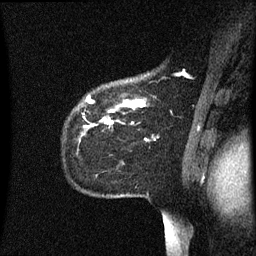
Breast MRI (dynamic contrast-enhanced), one sagittal slice; slice 48 of 60 in the series (ordered by position); dynamic contrast-enhanced series, image 2 of 3 at this slice position (ordered by acquisition); 1.5 T; TE 4.2 ms, TR 8.4 ms; 2.2 mm slice thickness; 256 × 256 image matrix, field of view 200 × 200 mm. Patient: female, 35 years. From the clinical record (not read from this slice): setting: breast cancer imaged before/during neoadjuvant chemotherapy; receptor status: HER2-positive.
Structures marked on this image (semi-automatically segmented with operator editing):
- analysis volume of interest (the breast-tissue region the enhancement analysis was run in; not a lesion): bounding box [x1, y1, x2, y2] px = [77, 78, 148, 155]
- tumour enhancement mask (voxels above the 70 % enhancement threshold inside the analysis volume of interest): [88, 98, 145, 125]